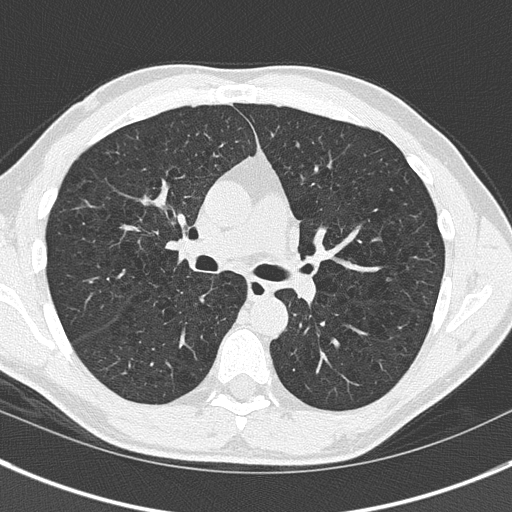
Low-dose screening chest CT, axial slice, baseline screening round, lung window (W 1500 / L -600 HU), lung (sharp) reconstruction kernel (B50f), slice 75 of 175 in the series. Male, age 56 years at enrolment. Current smoker at enrolment.
Lesion marked by an expert reader, bounding box (x1, y1, x2, y2) in pixels: (133, 187, 165, 221). The screening reader recorded 3 non-calcified nodules or masses ≥4 mm on this exam; which of them this box marks is not recorded. Official screen result: positive, change unspecified: nodule(s) >= 4 mm or enlarging nodule(s), mass(es), or other non-specific abnormalities suspicious for lung cancer. Lung cancer was diagnosed 228 days after this screen: non-small cell carcinoma, right upper lobe, stage IIIA (AJCC 6th edition), 21 mm at pathology.